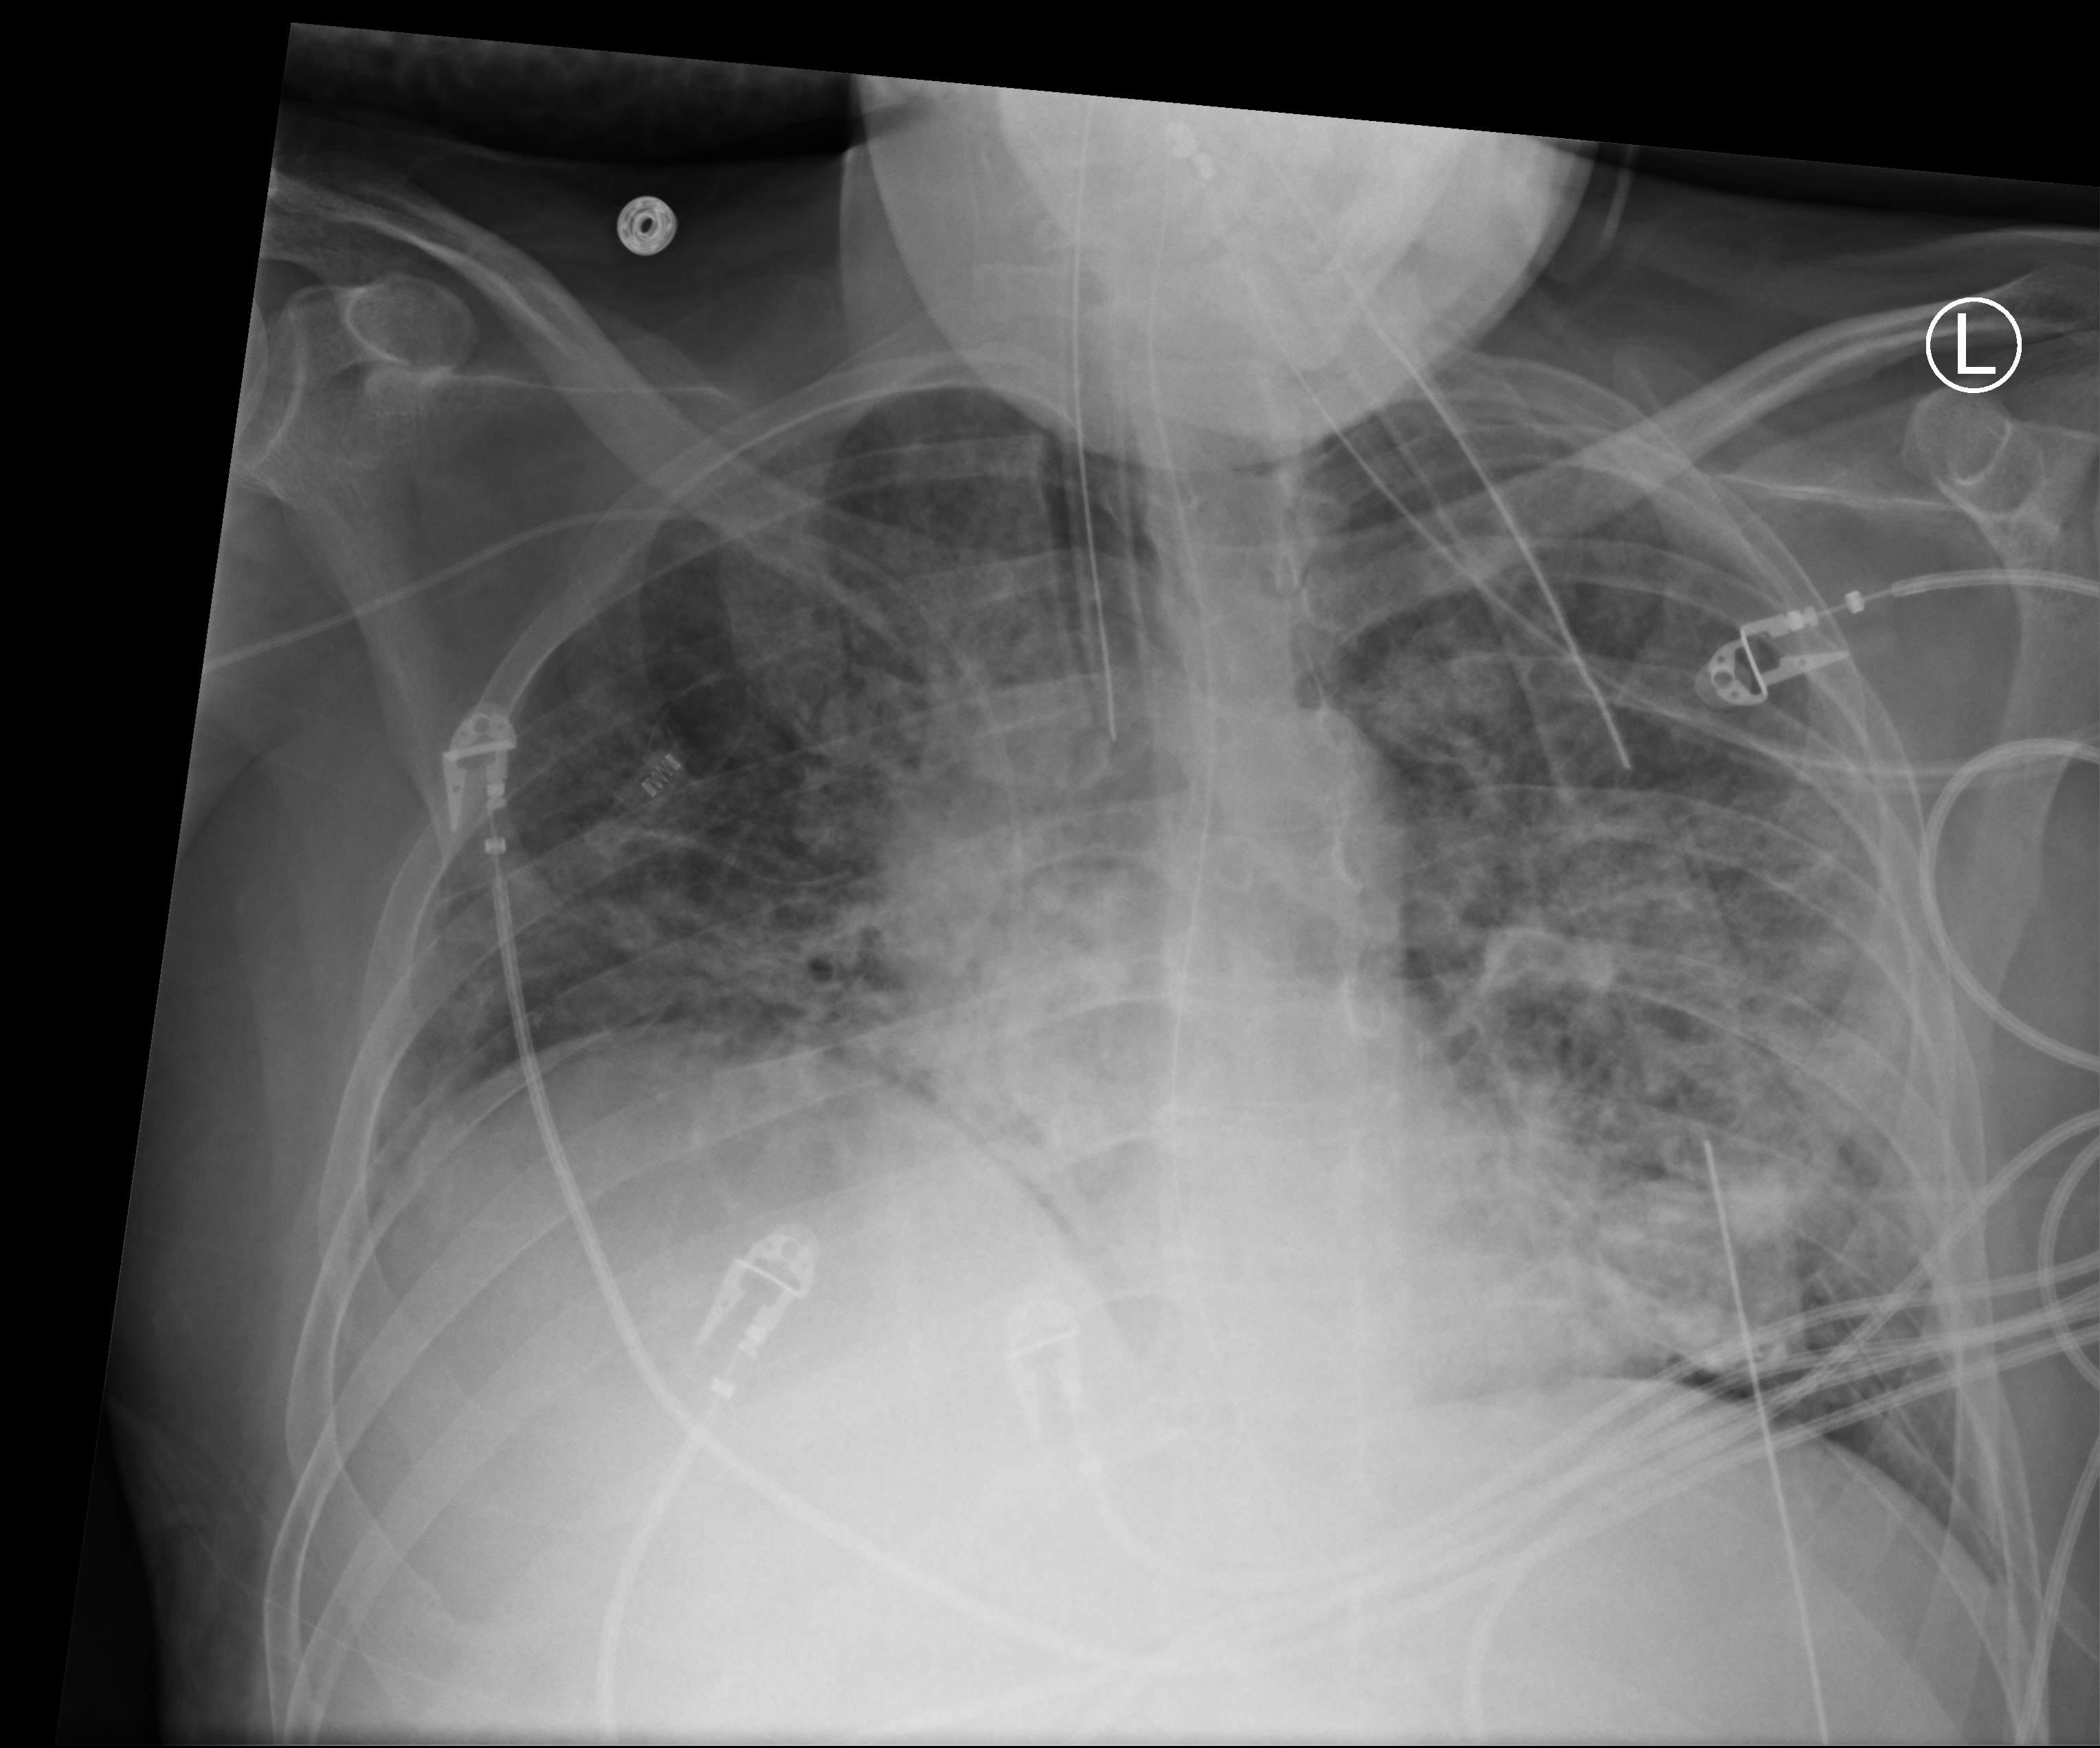
Portable chest radiograph. Male patient hospitalised with COVID-19, age 18–59 years.
Hospital-stay facts (about this admission, not read from this image; timing relative to this image not recorded):
- diabetes (admission record): no
- mechanically ventilated during this hospital stay: yes
- chronic kidney disease (admission record): no